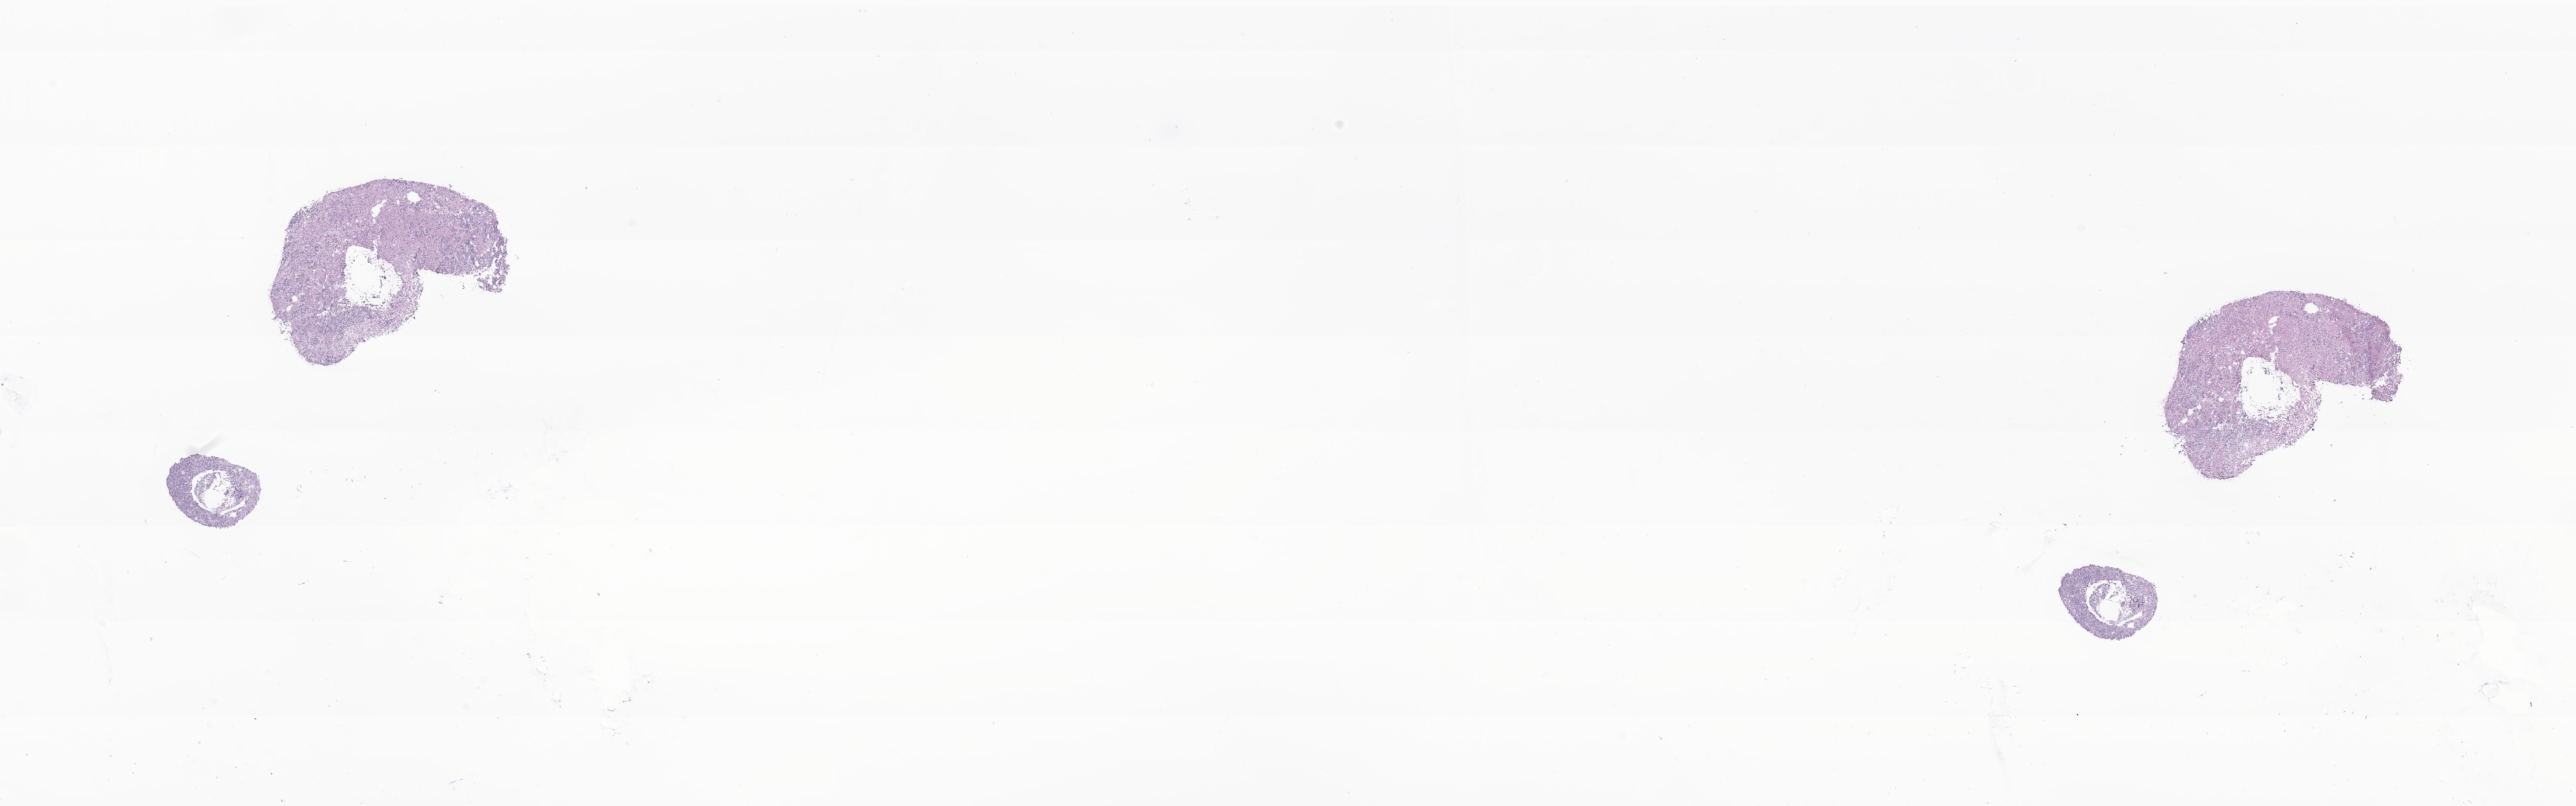
Digitized hematoxylin and eosin (H&E)-stained section of tumor tissue from the occipital lobe, whole scanned area (about 28.8 x 9.0 mm) shown as a low-resolution overview; cryosection (OCT / tissue freezing medium). Patient: female, age 164 months (13 years 8 months).
Diagnosis: Glioma, malignant.